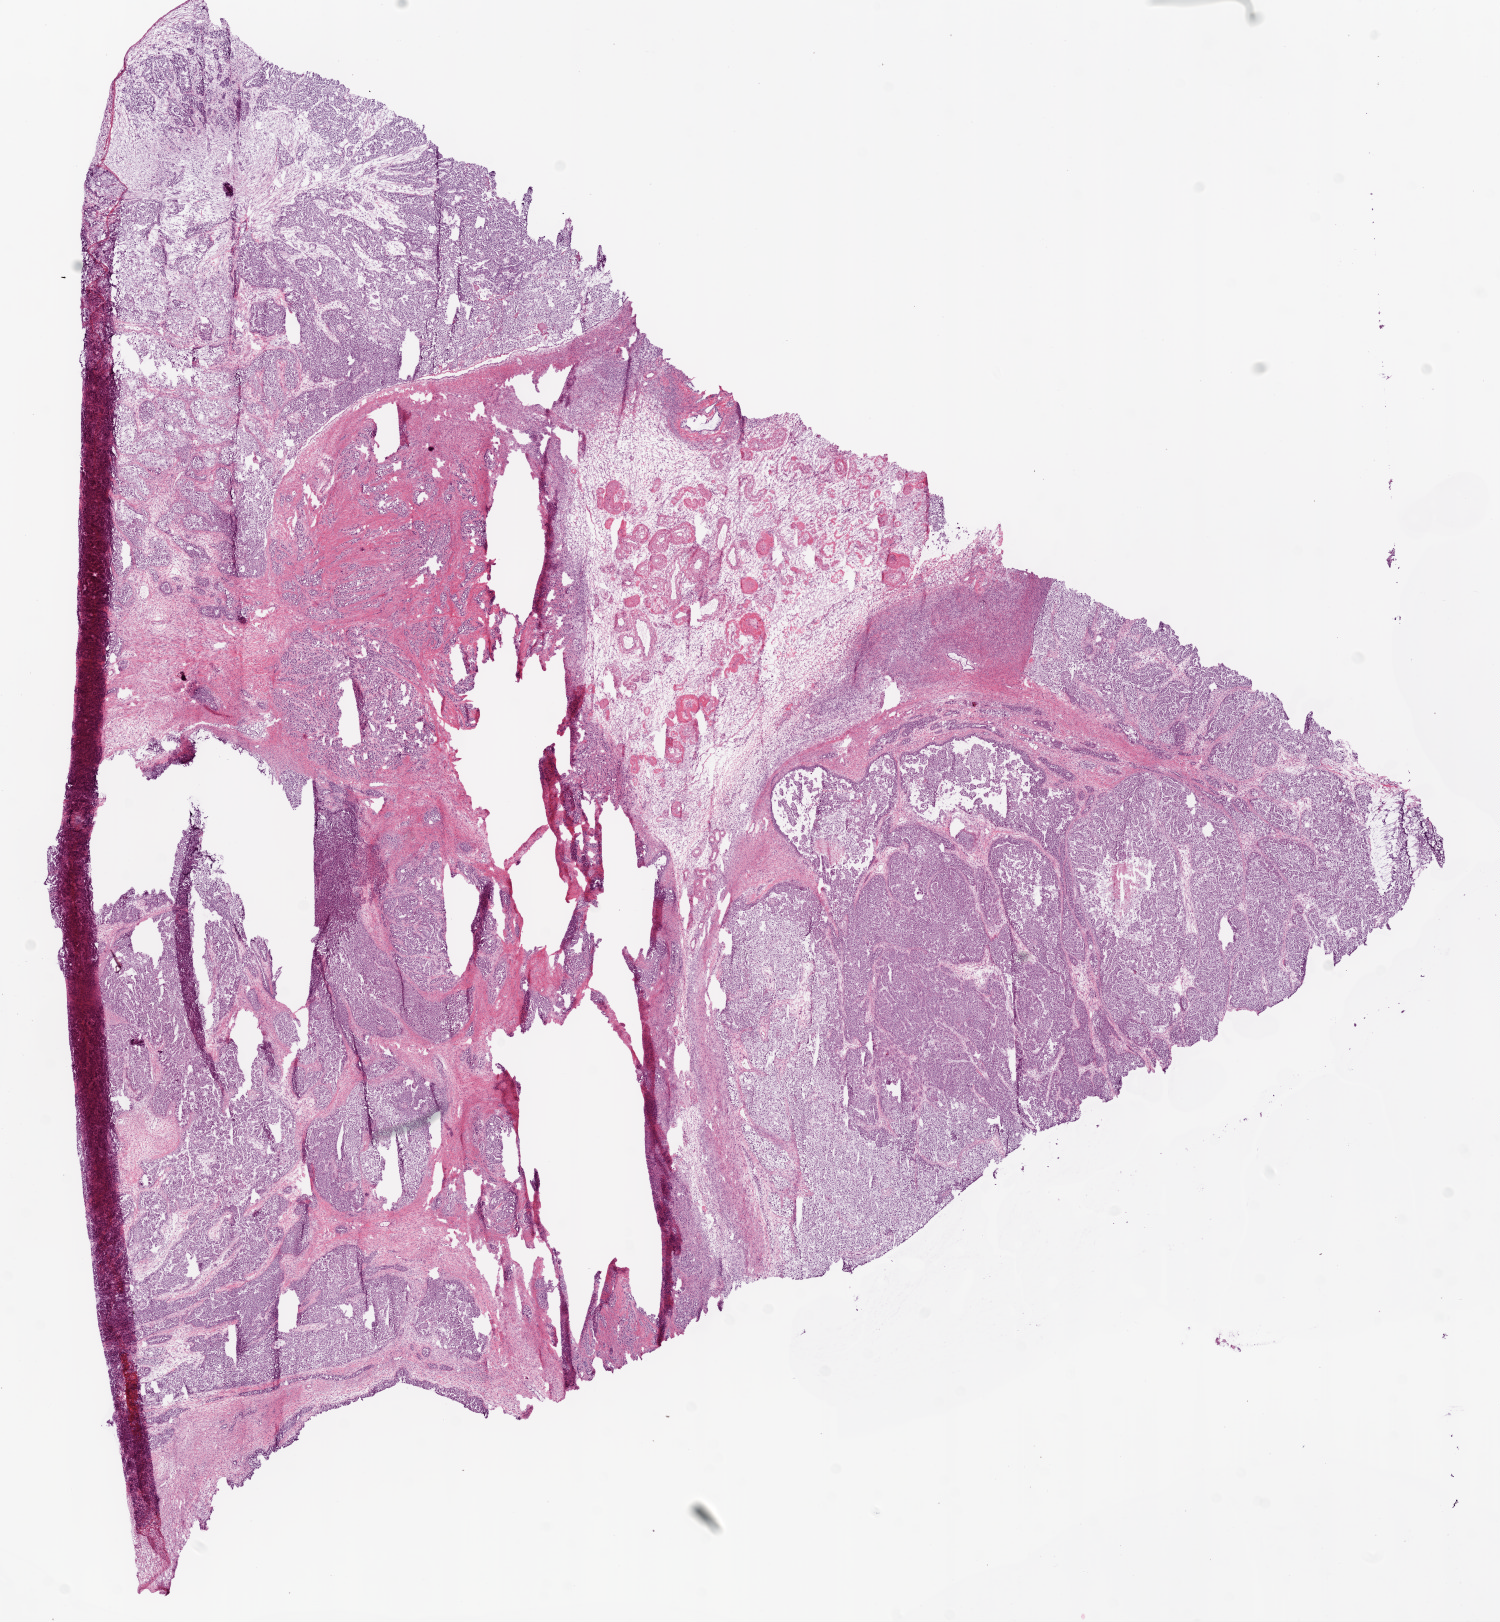
H&E-stained whole-slide image — a low-resolution overview of the entire scanned area, about 12.0 x 13.0 mm (from a 20x scan); frozen section from the bottom of the tissue portion; ovary, primary tumour sample. Female patient; age at initial diagnosis 66 years. Histologic grade: G3 (poorly differentiated). Pathologist review of this section (percent, as recorded): tumour cells 70%, tumour nuclei 80%, normal cells 15%, stromal cells 10%, necrosis 5%.
• FIGO stage: IIIC
• pathologic diagnosis: Serous cystadenocarcinoma, NOS